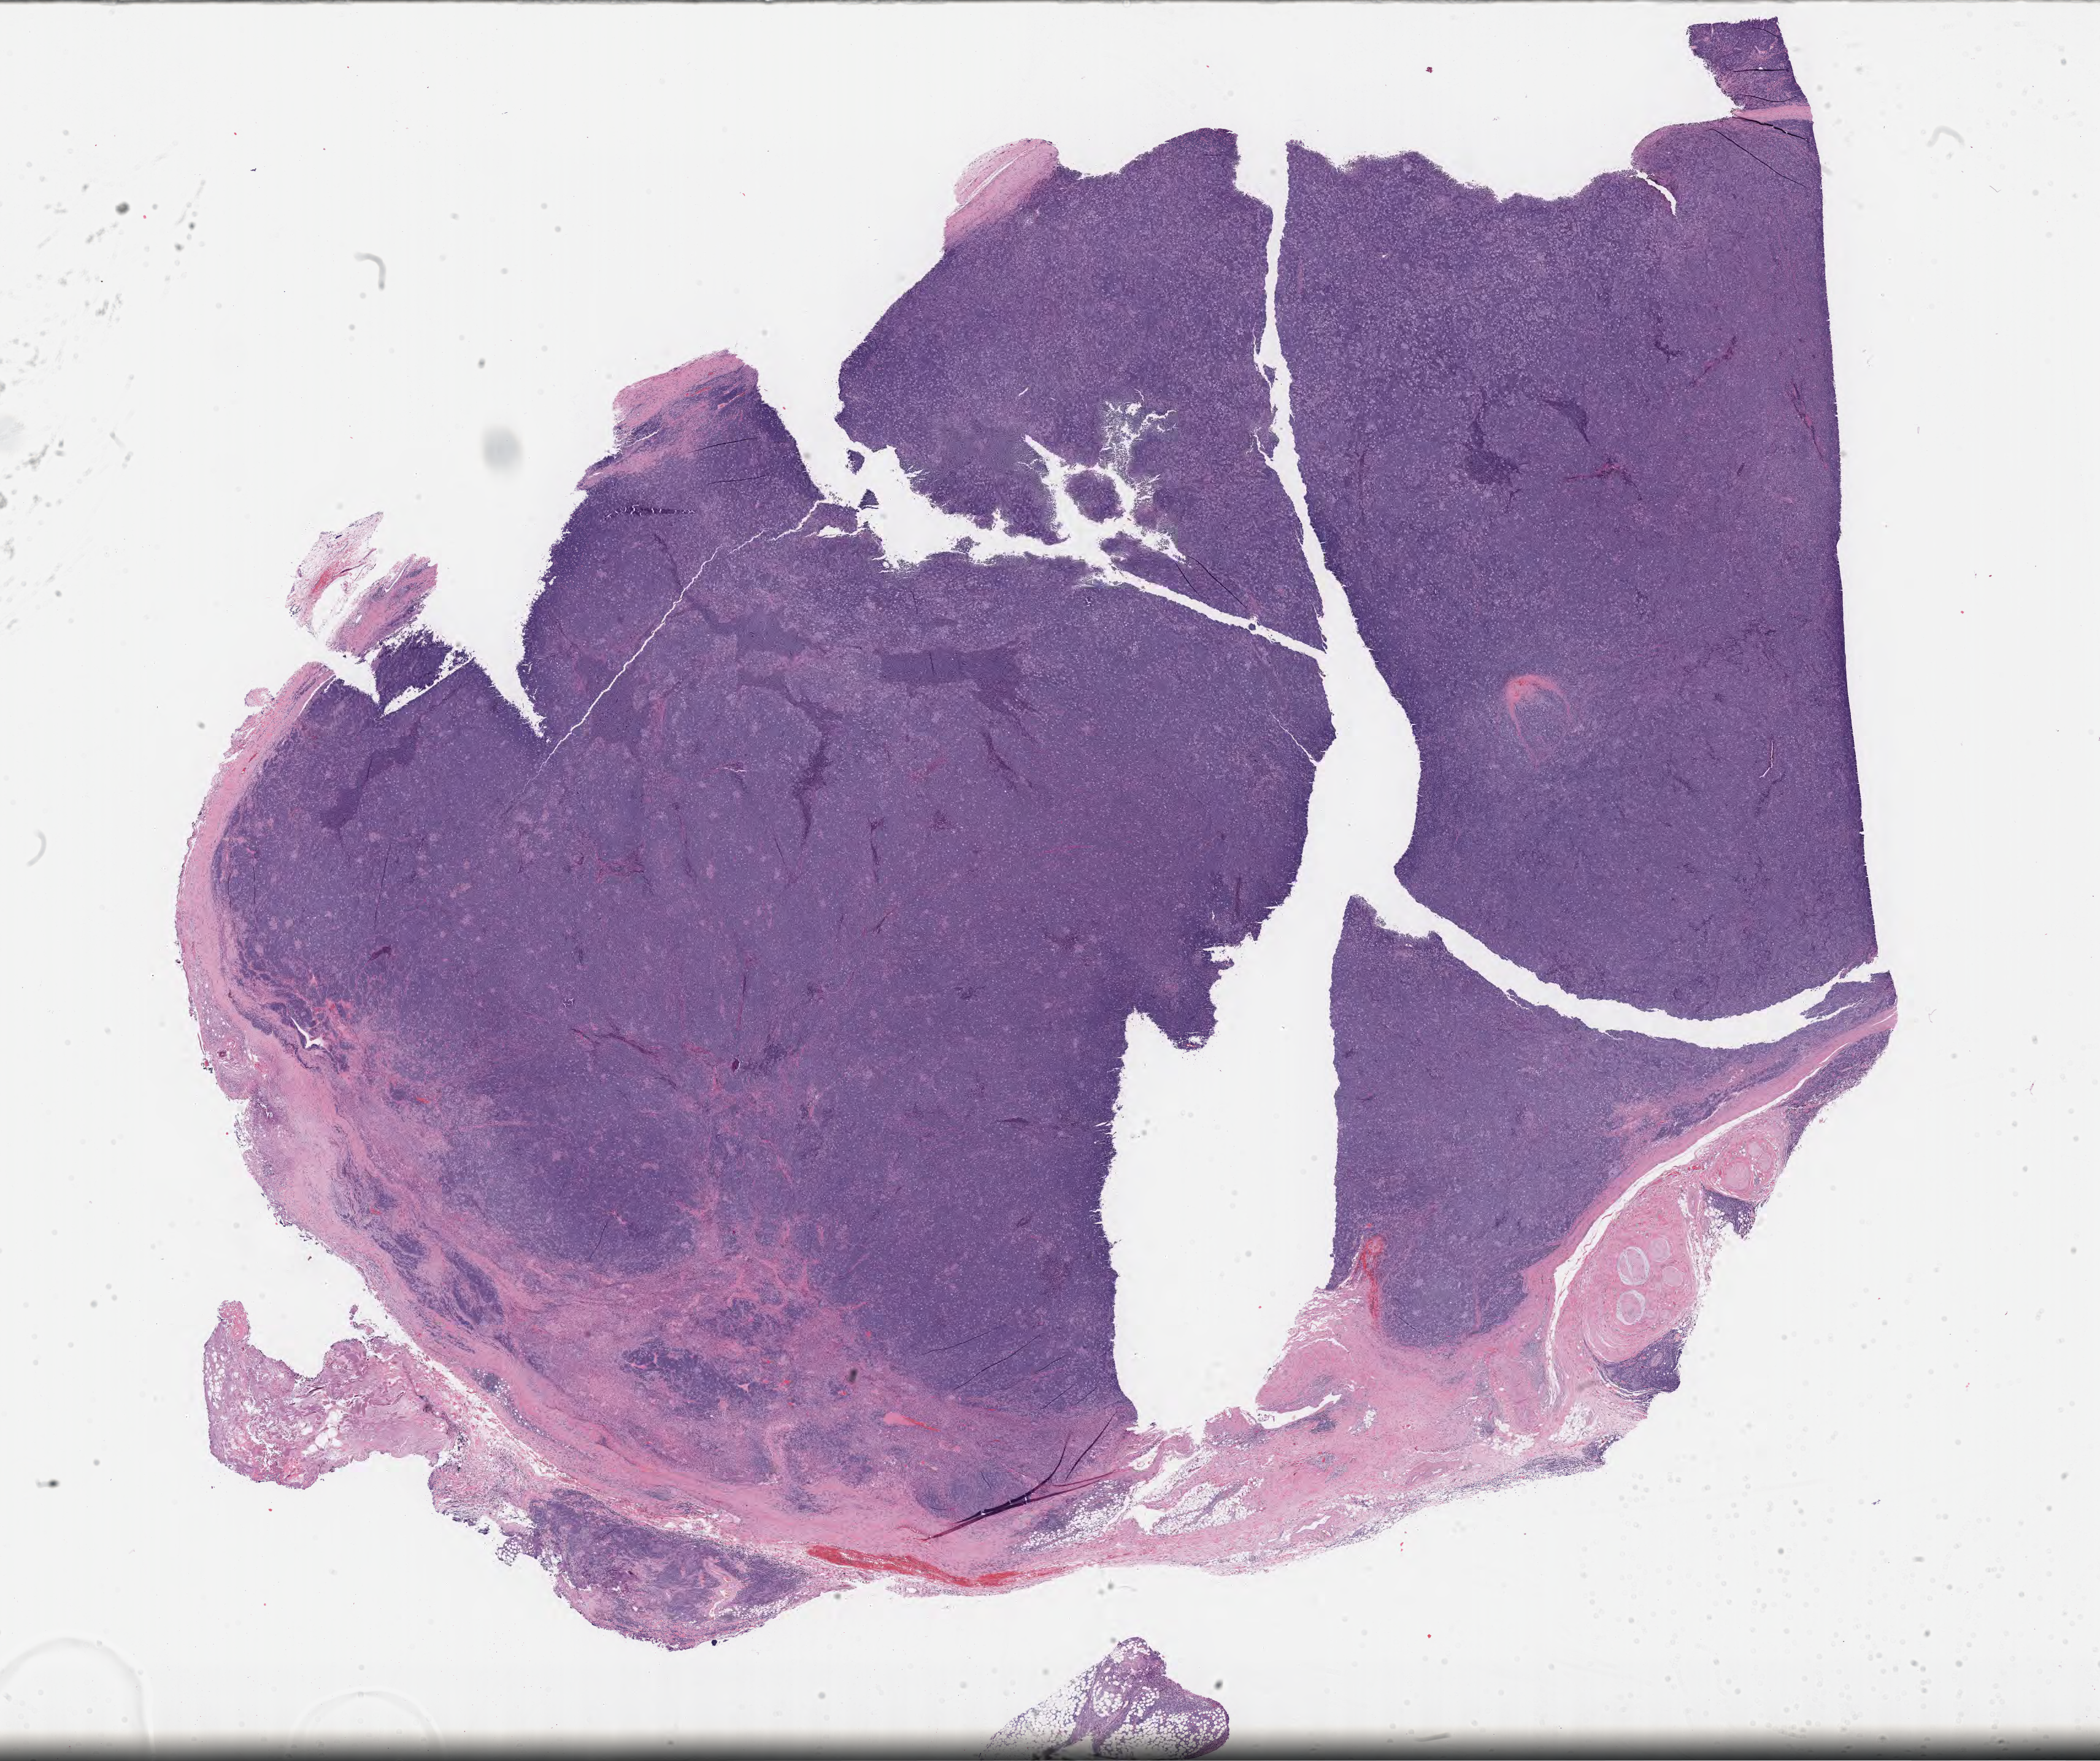
Digitized H&E-stained section, shown as a low-resolution overview of the whole scanned area (about 27.7 x 23.2 mm), tumor tissue. Male patient, aged 30.
Histologic diagnosis: Burkitt lymphoma, NOS.